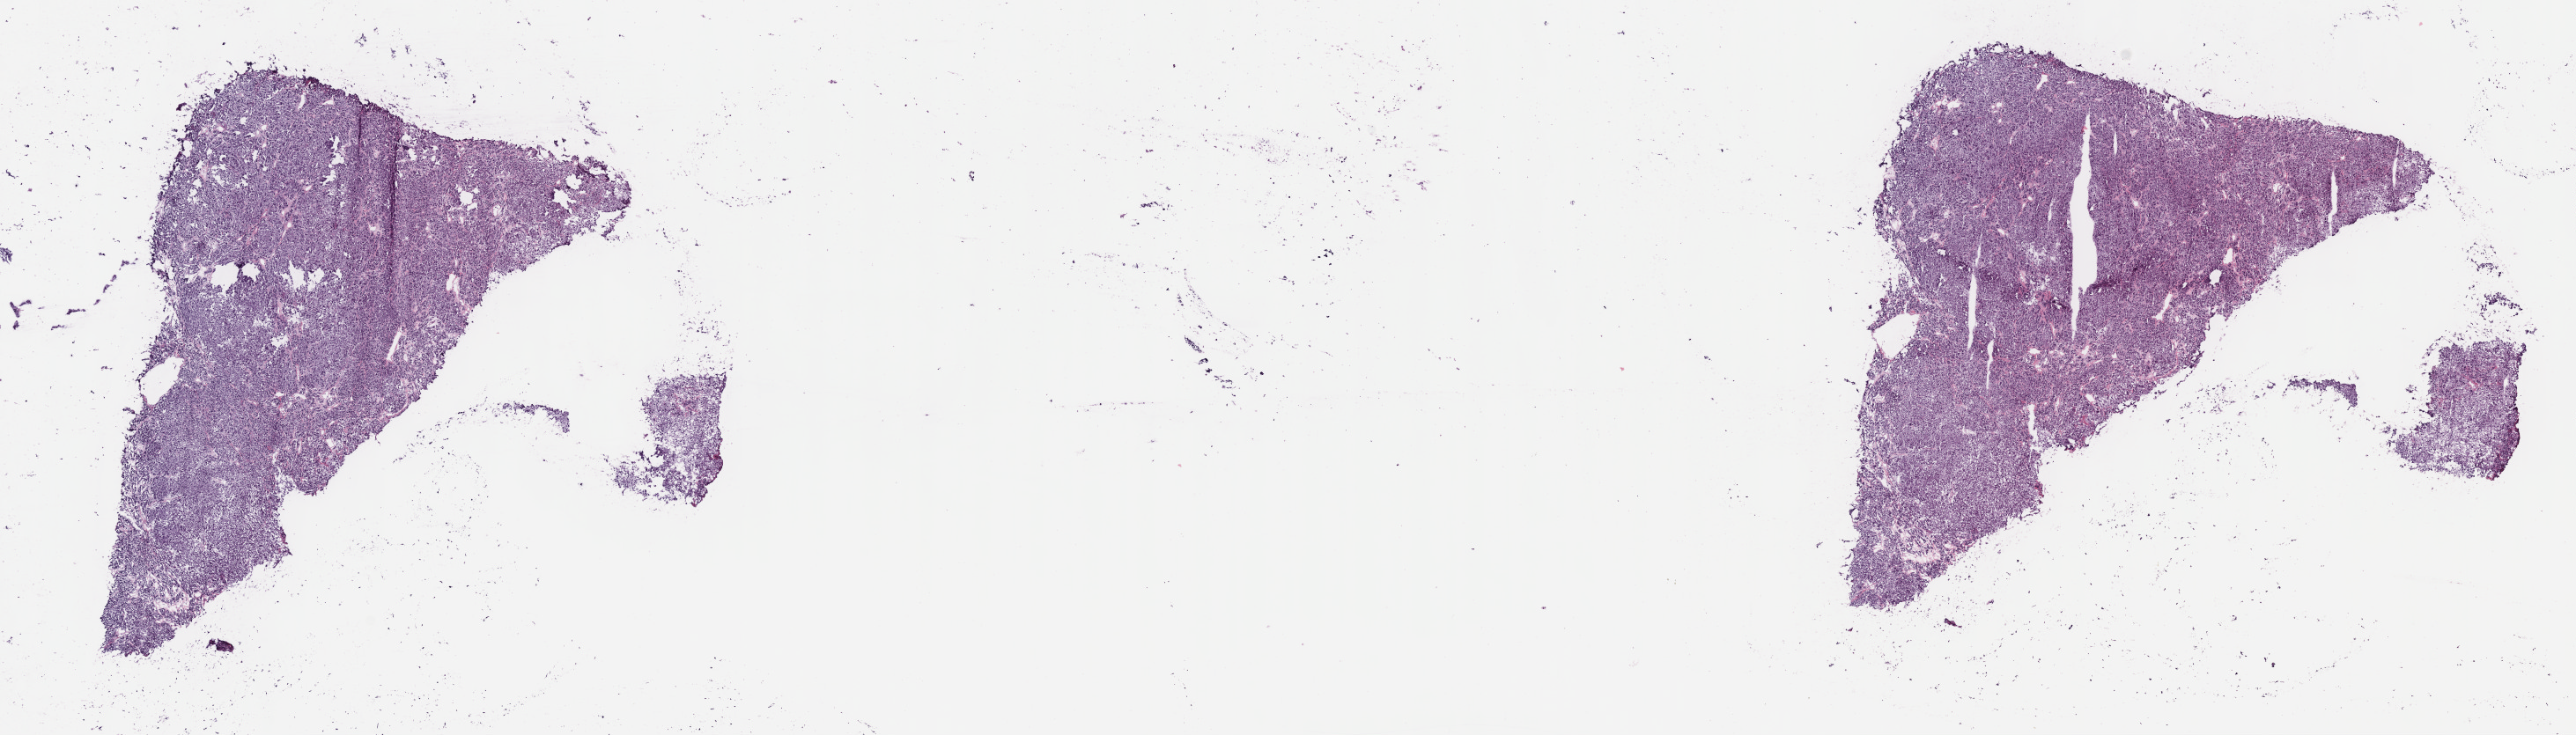
Digitized H&E-stained tissue section (whole slide), whole scanned area (about 23.7 x 6.8 mm) shown as a low-resolution overview, frozen section from the top of the tissue portion, primary tumour sample from the adrenal gland. Female, age 28 years at initial diagnosis. Composition of this section per pathologist review: tumour cells 80%, tumour nuclei 80%, normal cells 0%, stromal cells 20%, necrosis 0%. Inflammatory infiltration, as recorded: lymphocyte infiltration 2%, monocyte infiltration 1%, neutrophil infiltration 1%.
Histologic diagnosis: Medullary carcinoma, NOS (thyroid gland). AJCC pathologic stage: IVA (7th edition). Laterality: bilateral. TNM: T2 N1b MX.